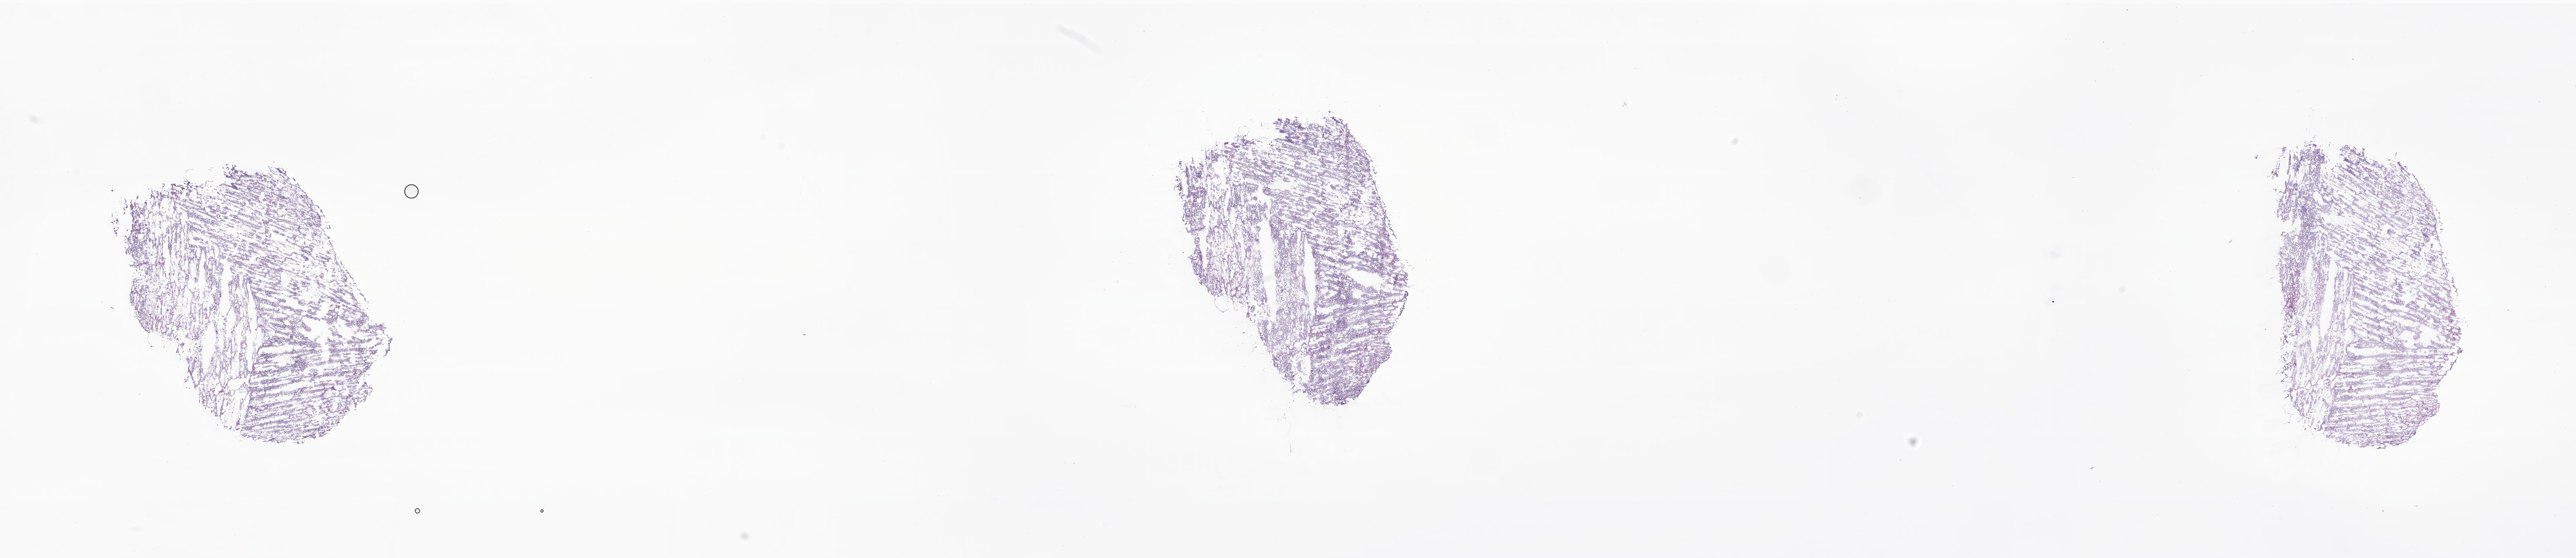
Digitized haematoxylin and eosin-stained section of tumor tissue from the brain — whole scanned area (about 42.1 x 9.1 mm) shown as a low-resolution overview; cryosection (OCT / tissue freezing medium). Patient: male, age 45 months.
Recorded diagnosis: Medulloblastoma, NOS.